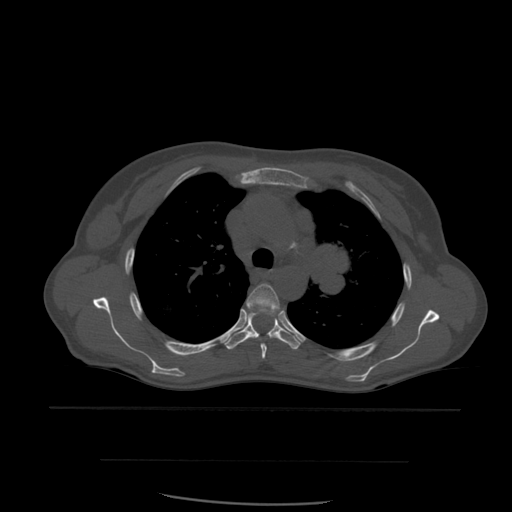
CT including the spine, one axial slice; position 417 of 574 along the scan axis; bone window (W 1800 / L 400 HU); 1.25 mm slice thickness; 512 × 512 image matrix. Patient age 48 years. From the clinical record (not read from this slice): primary cancer: lung.
Annotated regions visible in this slice (semi-automatic segmentation, software-assisted and operator-edited):
- T4 vertebra: bounding box (x1, y1, x2, y2) in pixels: (247, 284, 281, 360)
- T5 vertebra: (225, 311, 301, 350)